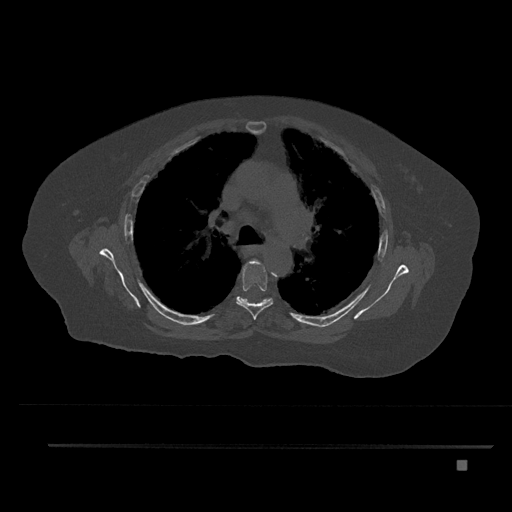
CT including the spine, one axial slice. Slice 564 of 797 in the series (ordered by position). Reconstruction kernel Br40s/3. Bone window (W 1800 / L 400 HU). 0.5 mm slice thickness. 512 × 512 image matrix, field of view 437 × 437 mm. Female patient, age 76 years. From the clinical record (not read from this slice): primary cancer: lung; vertebrae with lytic lesions (as recorded): T11, L3.
Outlined on this slice (semi-automatically segmented with operator editing):
- T5 vertebra: bounding box (x1, y1, x2, y2) in pixels: (236, 259, 273, 320)
- T6 vertebra: (236, 297, 271, 304)